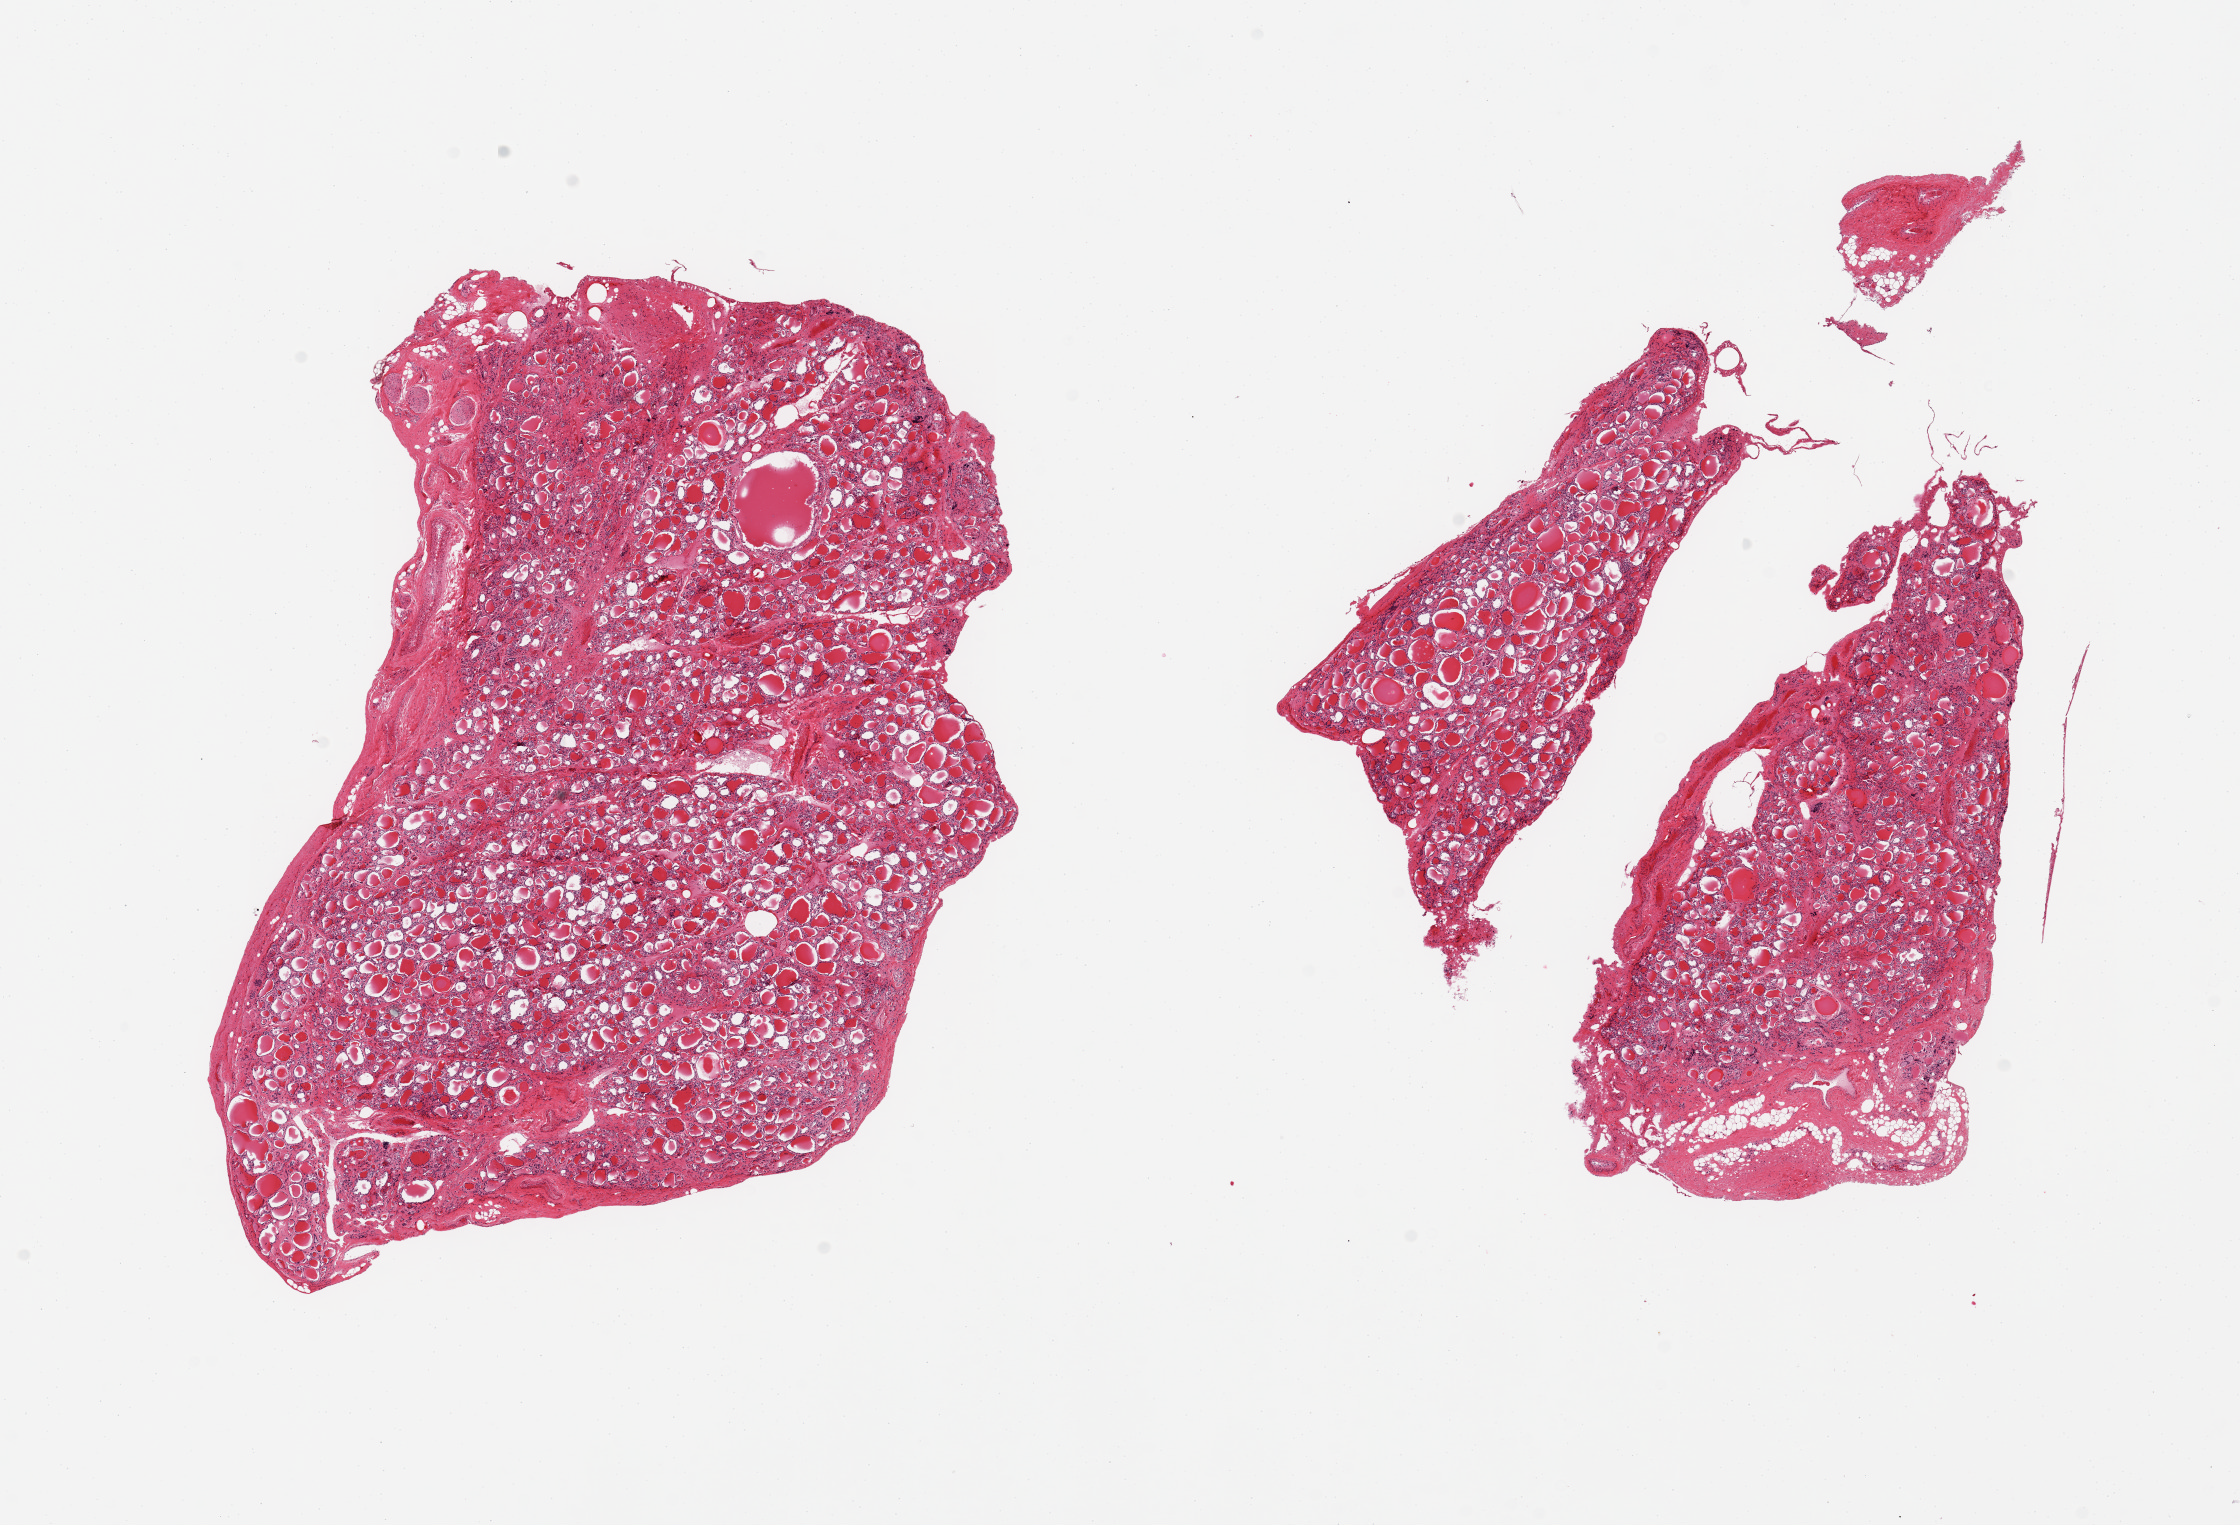
H&E whole-slide image — a low-resolution overview of the entire scanned area, about 17.7 x 12.1 mm (from a 20x scan). PAXgene-fixed paraffin-embedded (PFPE) section. Section of thyroid (target tissue). Donor tissue sample. Donor: female.
Review note (as recorded): 2 pieces, mild goiter, ~1mm colloid cyst.